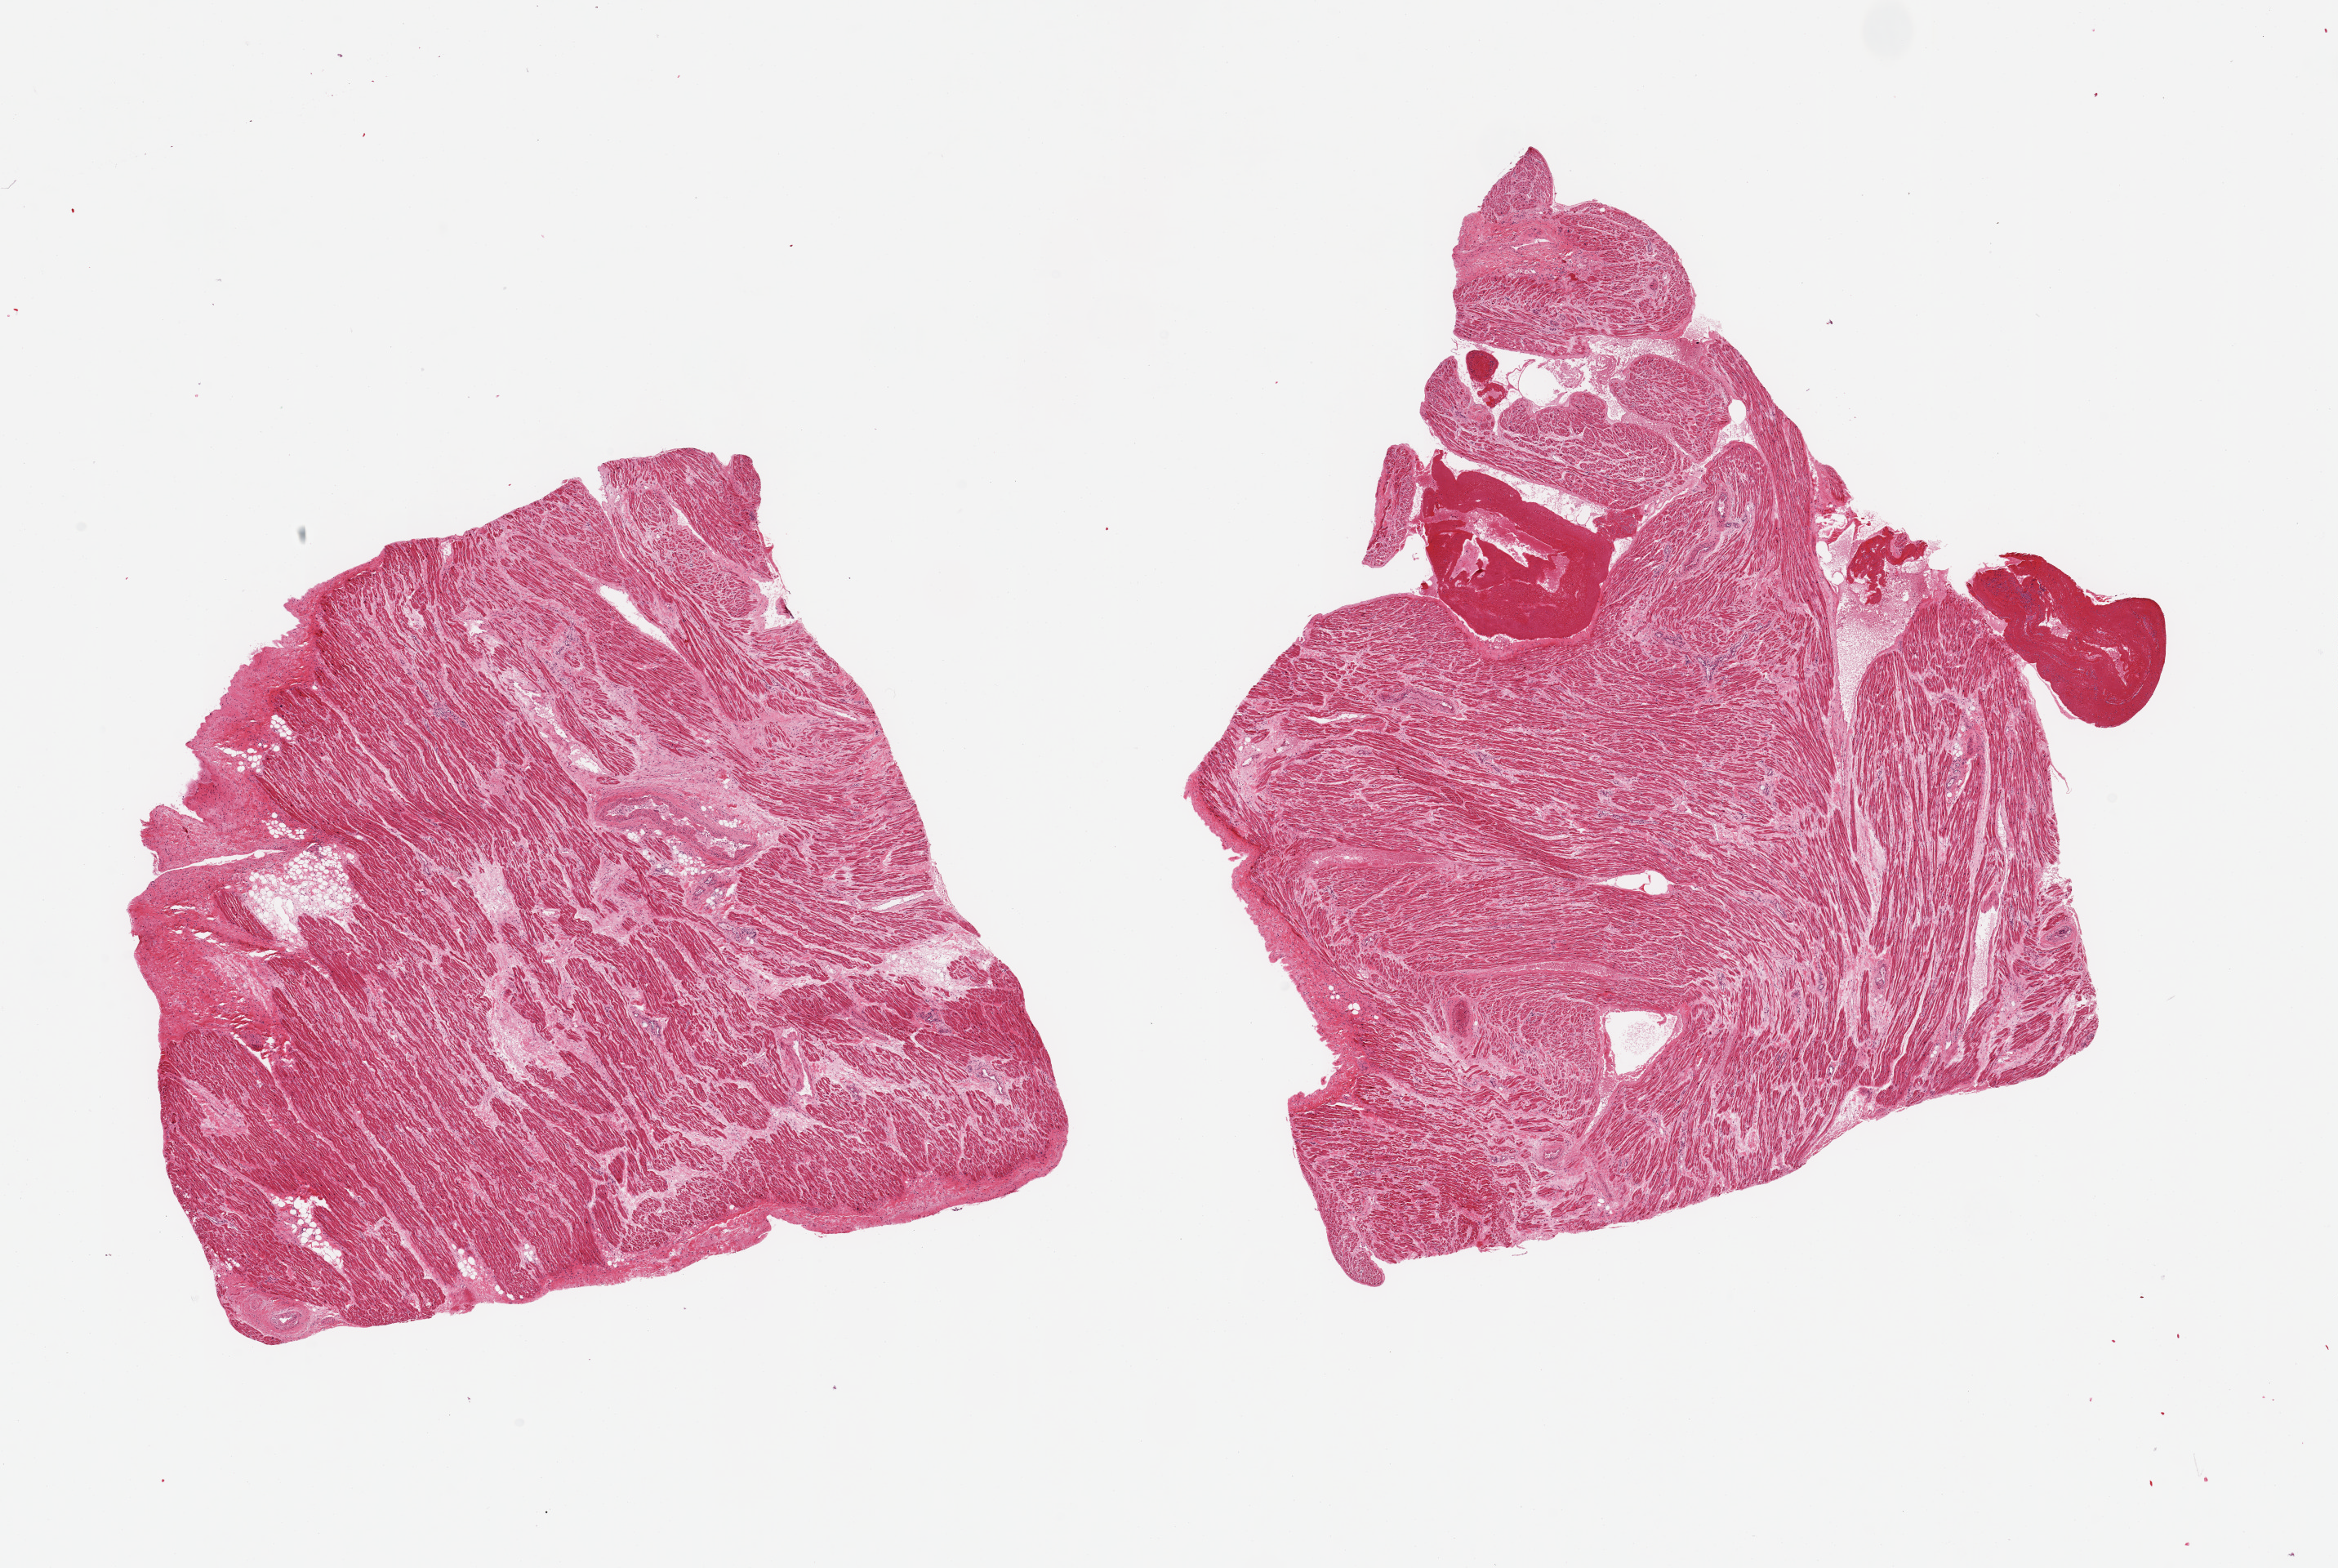
Digitized H&E-stained section — shown as a low-resolution overview of the whole scanned area (about 22.6 x 15.2 mm), PAXgene-fixed paraffin-embedded (PFPE) section, sampled site (target tissue): auricular appendage, tissue donor sample. Male donor.
Review note (as recorded): 2 pieces, no abnormalities.